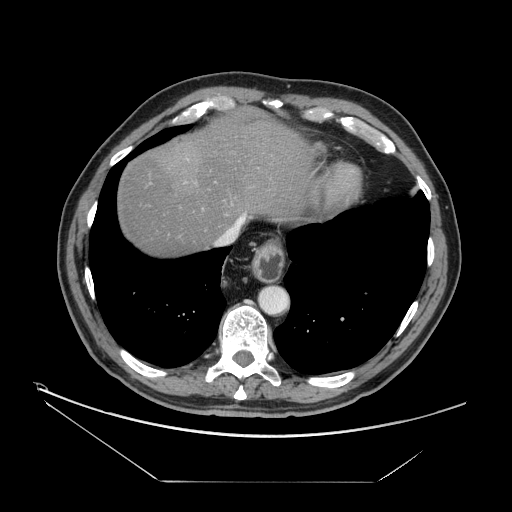
Contrast-enhanced abdominal CT, one axial slice. Position 140 of 161 along the scan axis. 120 kVp. Intravenous contrast given. Soft-tissue window (W 400 / L 40 HU). 512 × 512 image matrix. Male patient, age 65 years. From the clinical record (not read from this slice): diagnosis: colorectal cancer liver metastases, imaged before liver resection; multiple liver metastases: yes; largest metastasis: 4.2 cm.
Annotated regions visible in this slice (outlined manually by an expert reader):
- hepatic veins: bounding box <220,215,246,243> (left, top, right, bottom; pixels)
- liver: <117,110,312,255>
- planned liver remnant (the part of the liver to remain after resection): <117,111,313,255>